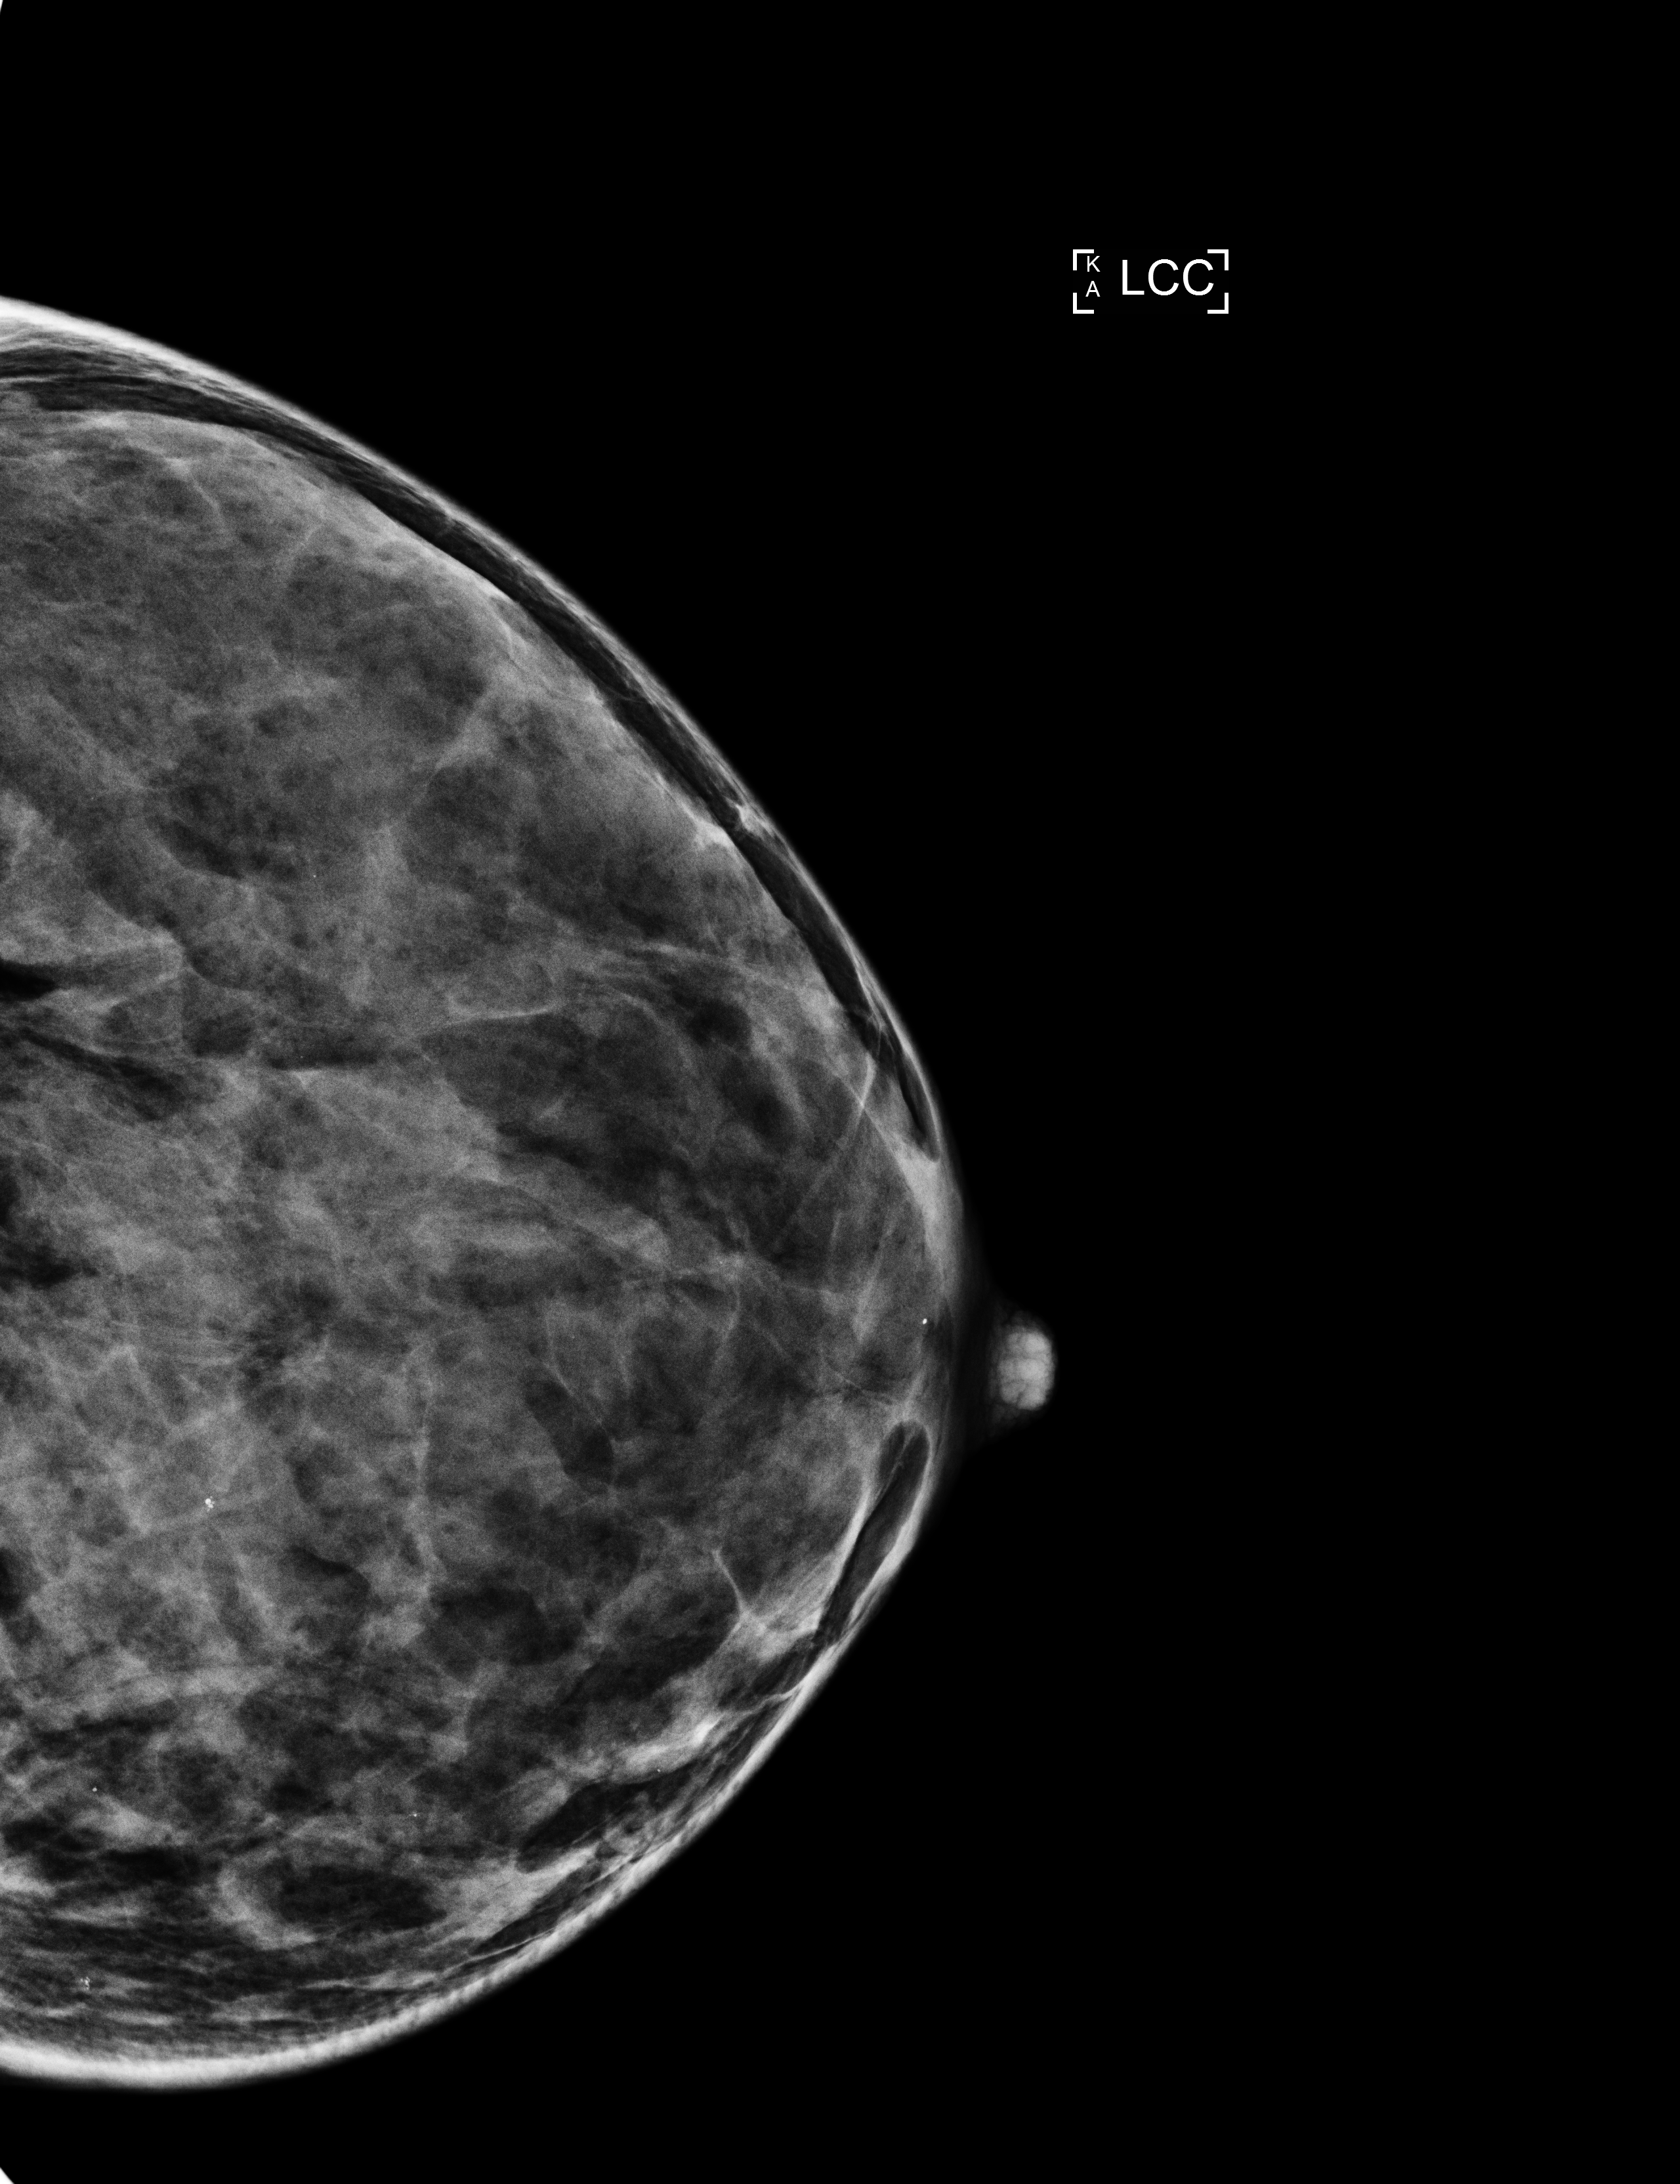
Full-field digital mammogram (FFDM), left breast, CC view, screening examination. Patient aged 41 years (female).
- breast density at the screening exam (both breasts): extremely dense (BI-RADS density category d)
- final BI-RADS category for the screening round (tomosynthesis exam, both breasts): category 2
- recall: no recall after this screen